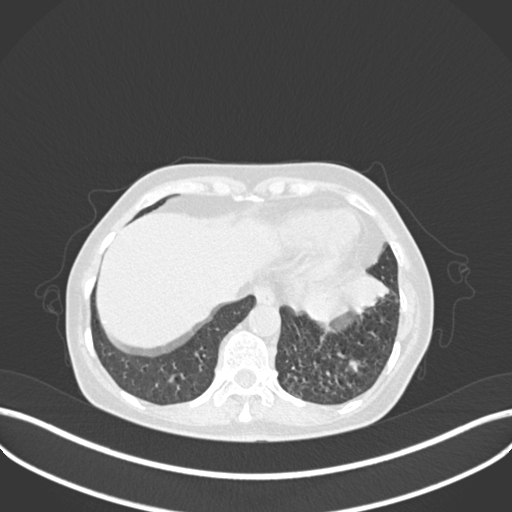
Chest CT, one axial slice. Slice 51 of 270 in the series (ordered by position). Reconstruction kernel B30f. 120 kVp. Lung window (W 1500 / L -600 HU). 512 × 512 image matrix, field of view 400 × 400 mm. Female patient, age 63 years. Case-level facts recorded for this patient, not image findings: clinical TNM (as recorded): T1b N0 M0.
Structures marked on this image (bounding box drawn by a radiologist):
- lung tumour (recorded histology: adenocarcinoma): bounding box (x1, y1, x2, y2) in pixels: (286, 265, 389, 325)